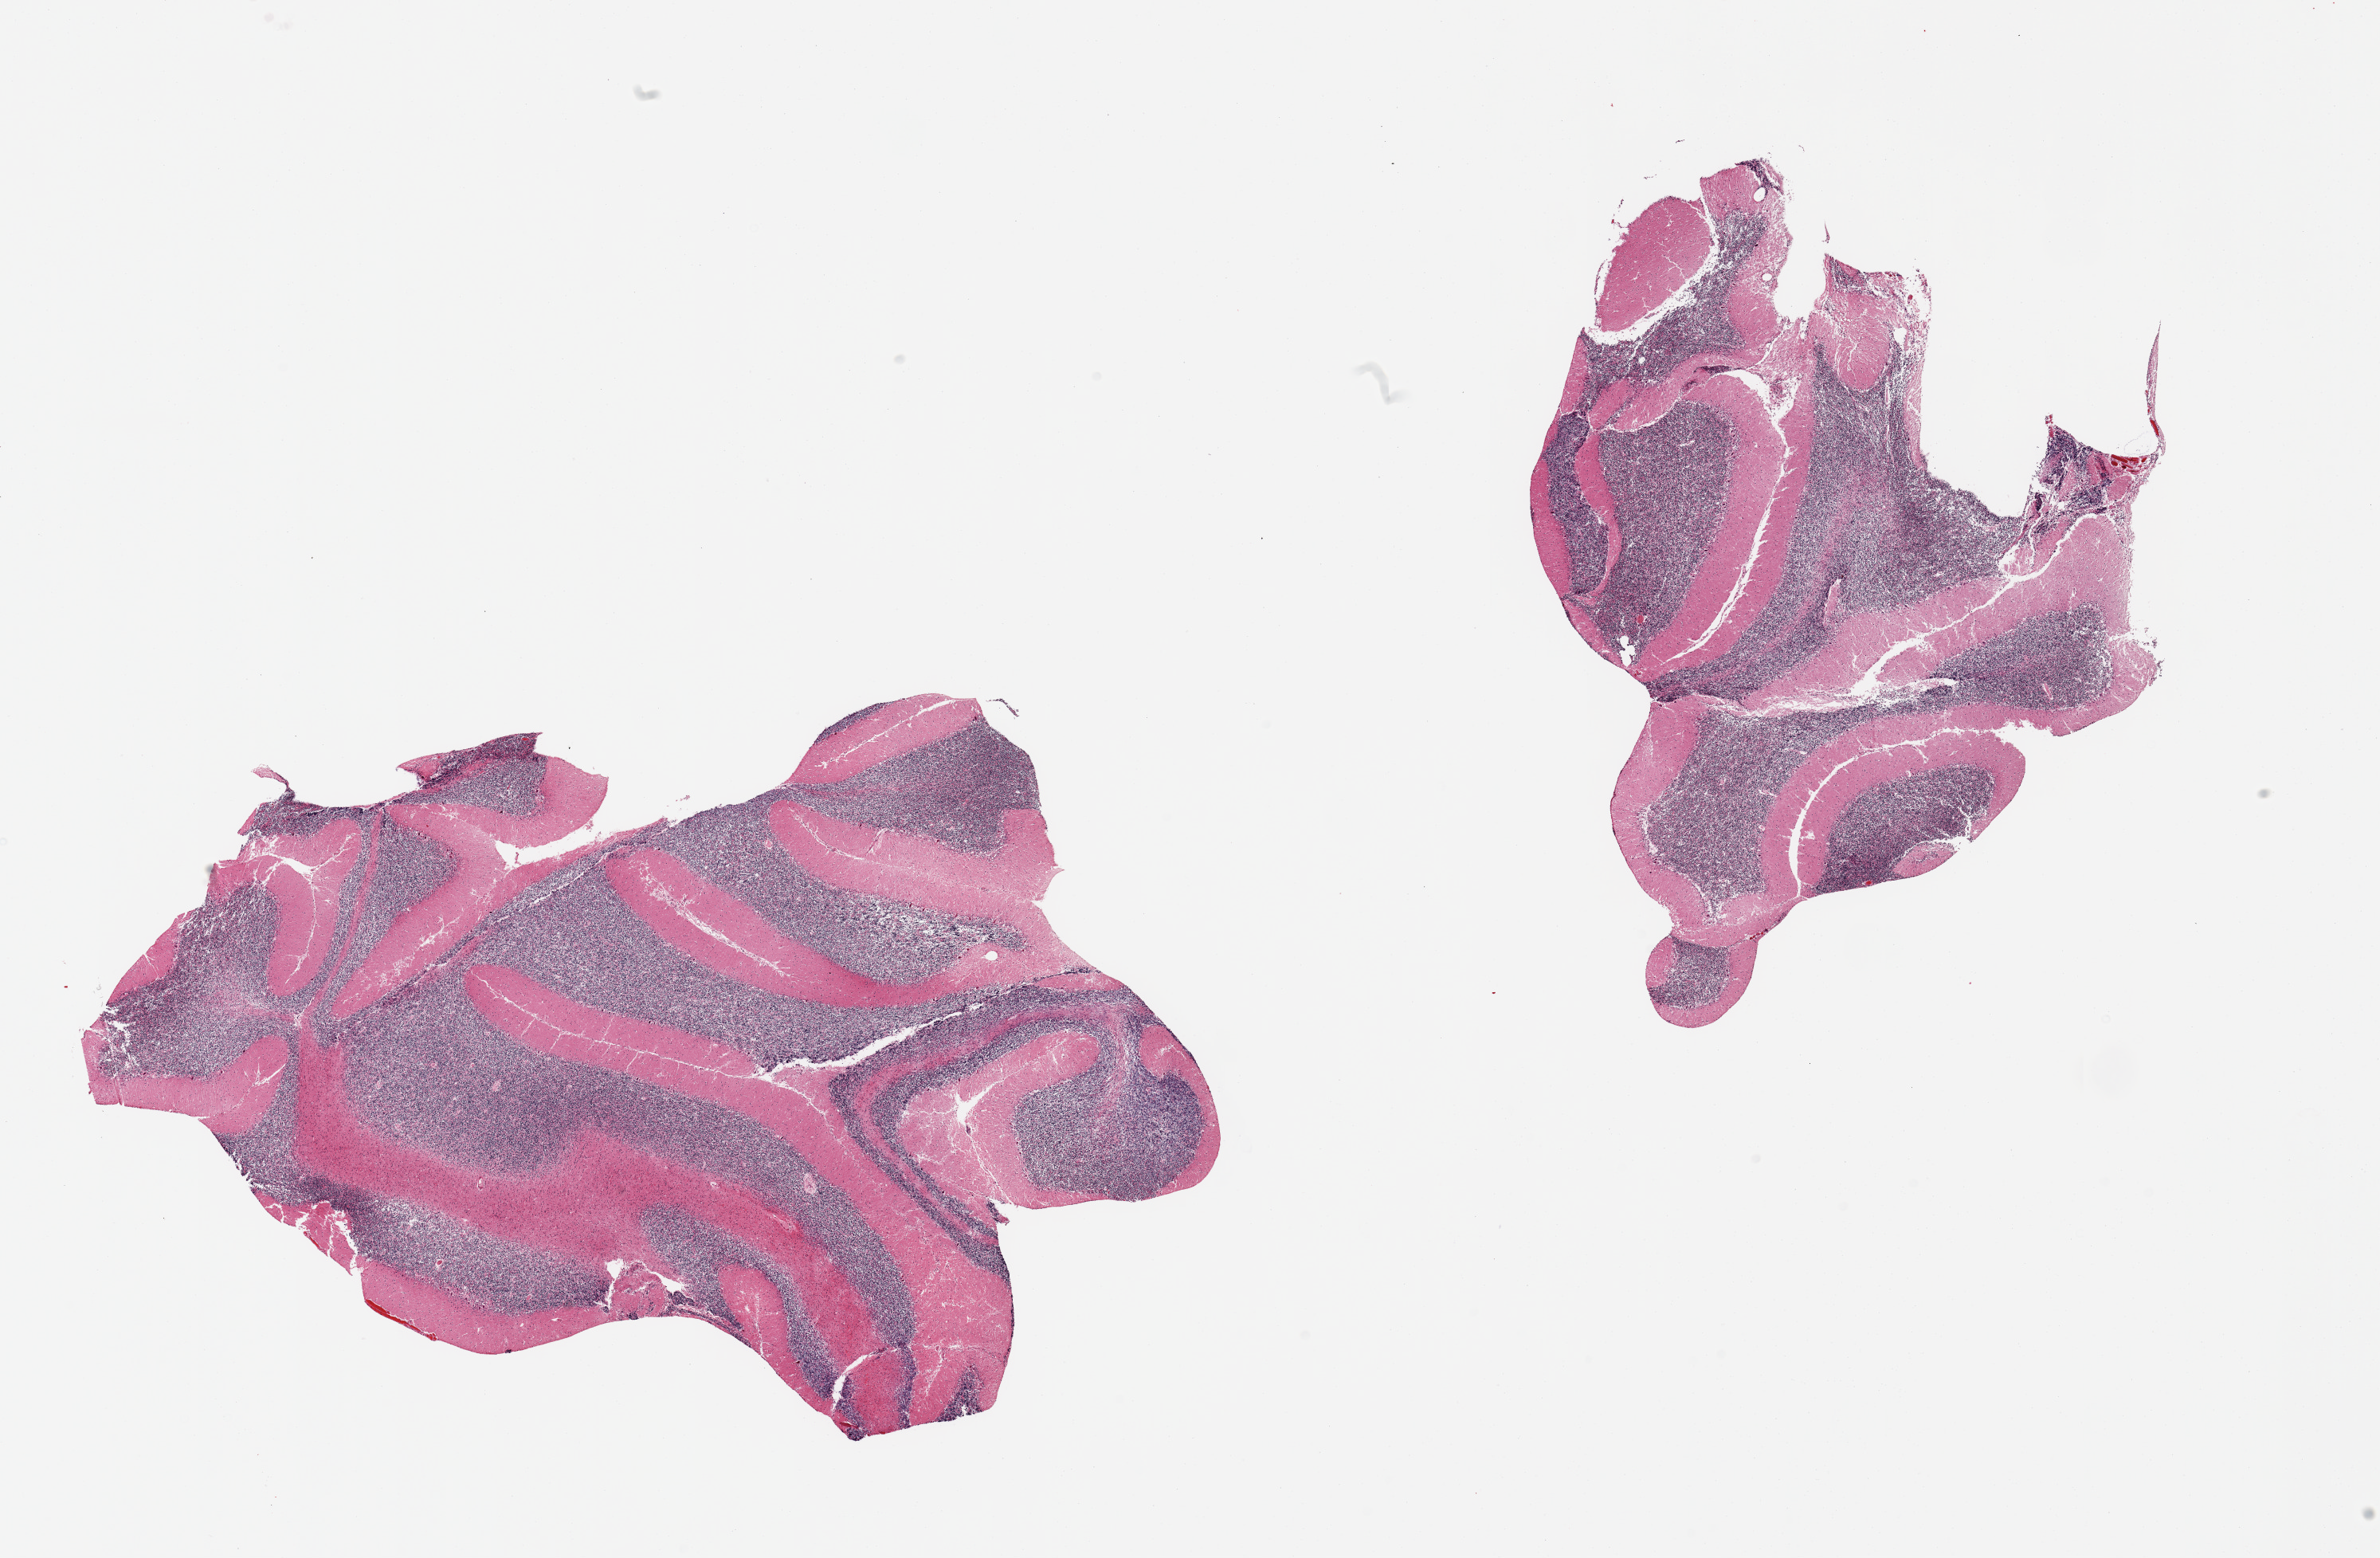
Haematoxylin and eosin whole-slide image — shown as a low-resolution overview of the whole scanned area (about 23.6 x 15.5 mm, slide scanned at 20x), PAXgene-fixed, paraffin-embedded tissue, target tissue: cerebellum, donor tissue sample.
- pathologist's review note for this sample: 2 pieces